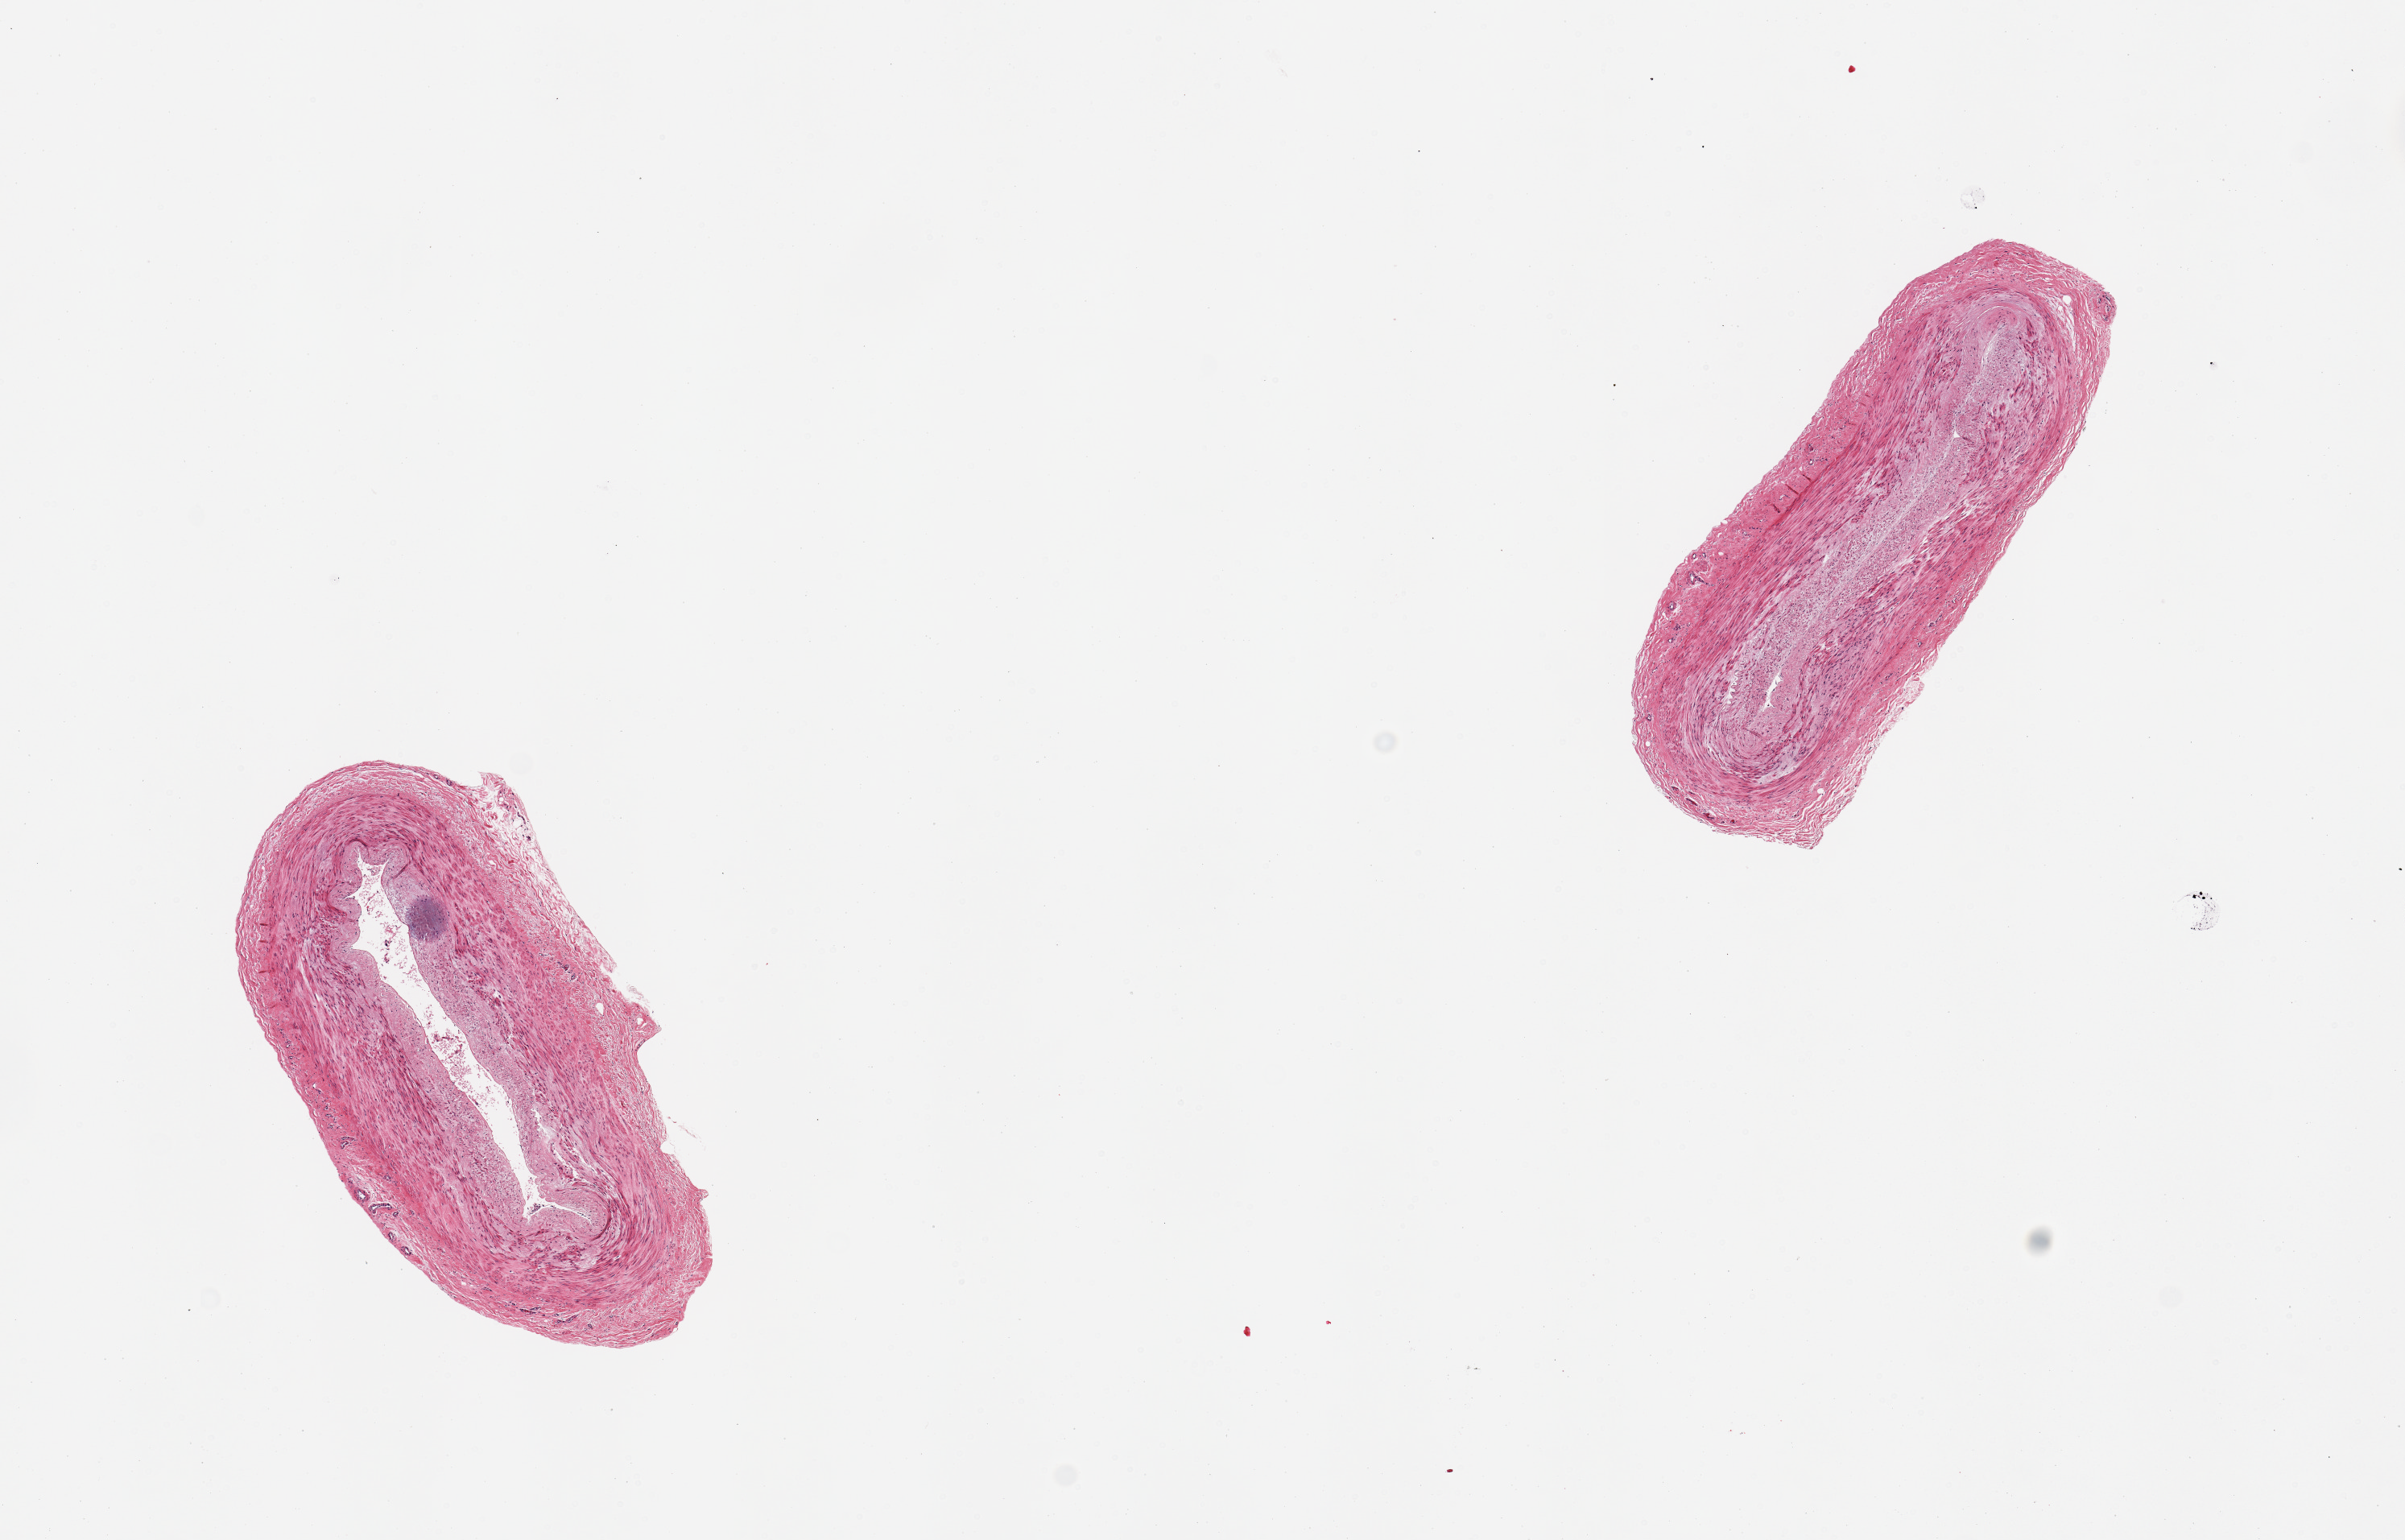
Whole-slide image, H&E stain, shown as a low-resolution overview of the whole scanned area (about 11.8 x 7.6 mm, from a 20x scan); PAXgene-fixed, paraffin-embedded tissue; sampled site (target tissue): tibial artery; donor tissue sample. Donor: male.
• review note (as recorded): 2 pieces; intimal thickening/early plaque formation